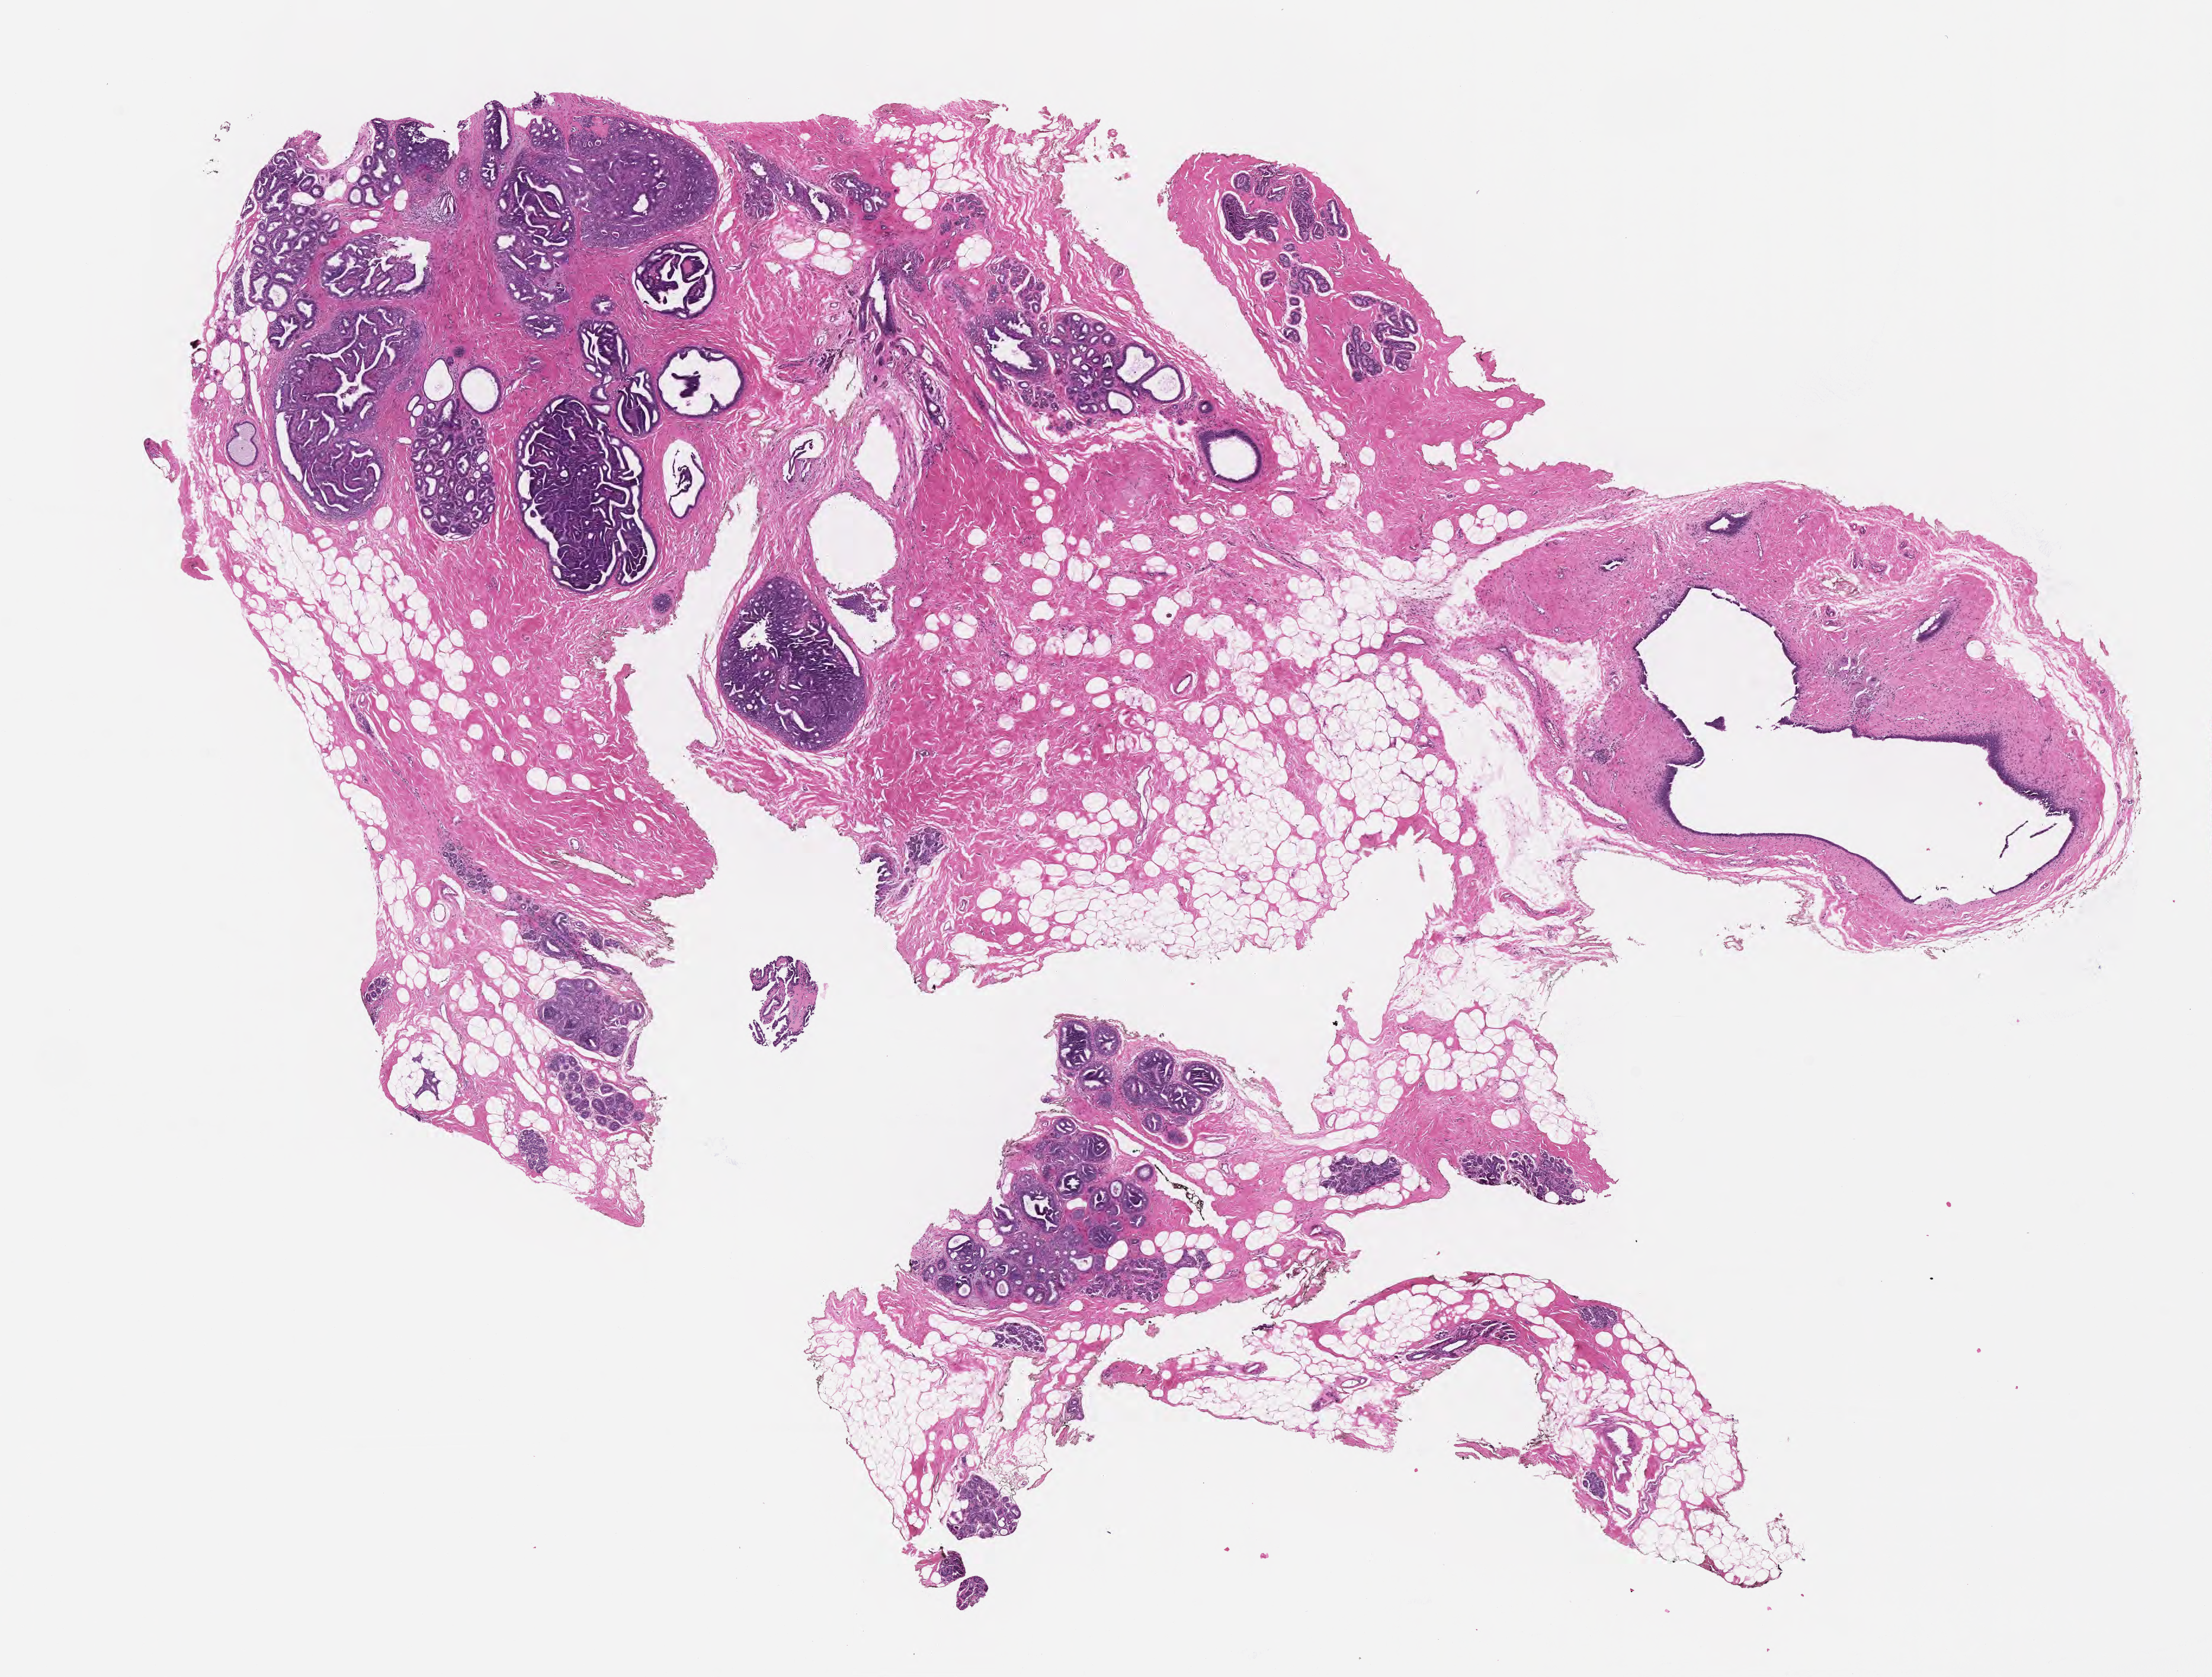
Whole-slide image, haematoxylin and eosin stain, a low-resolution overview of the entire scanned area, about 15.1 x 11.4 mm, formalin-fixed, paraffin-embedded (FFPE) tissue, premalignant lesion from a patient with intraductal carcinoma, noninfiltrating, NOS, anatomic site: breast. Female, age 49 years at initial diagnosis. Composition of this section per pathologist review: tumor cells 55%, tumor nuclei 55%, stromal cells 10%, necrosis 0%, normal cells 35%. Inflammatory infiltration, as recorded: lymphocyte infiltration 2%, monocyte infiltration 1%, neutrophil infiltration 3%.
This section: sample classed premalignant; the patient's recorded diagnosis is given above. Section: top of the tissue portion.